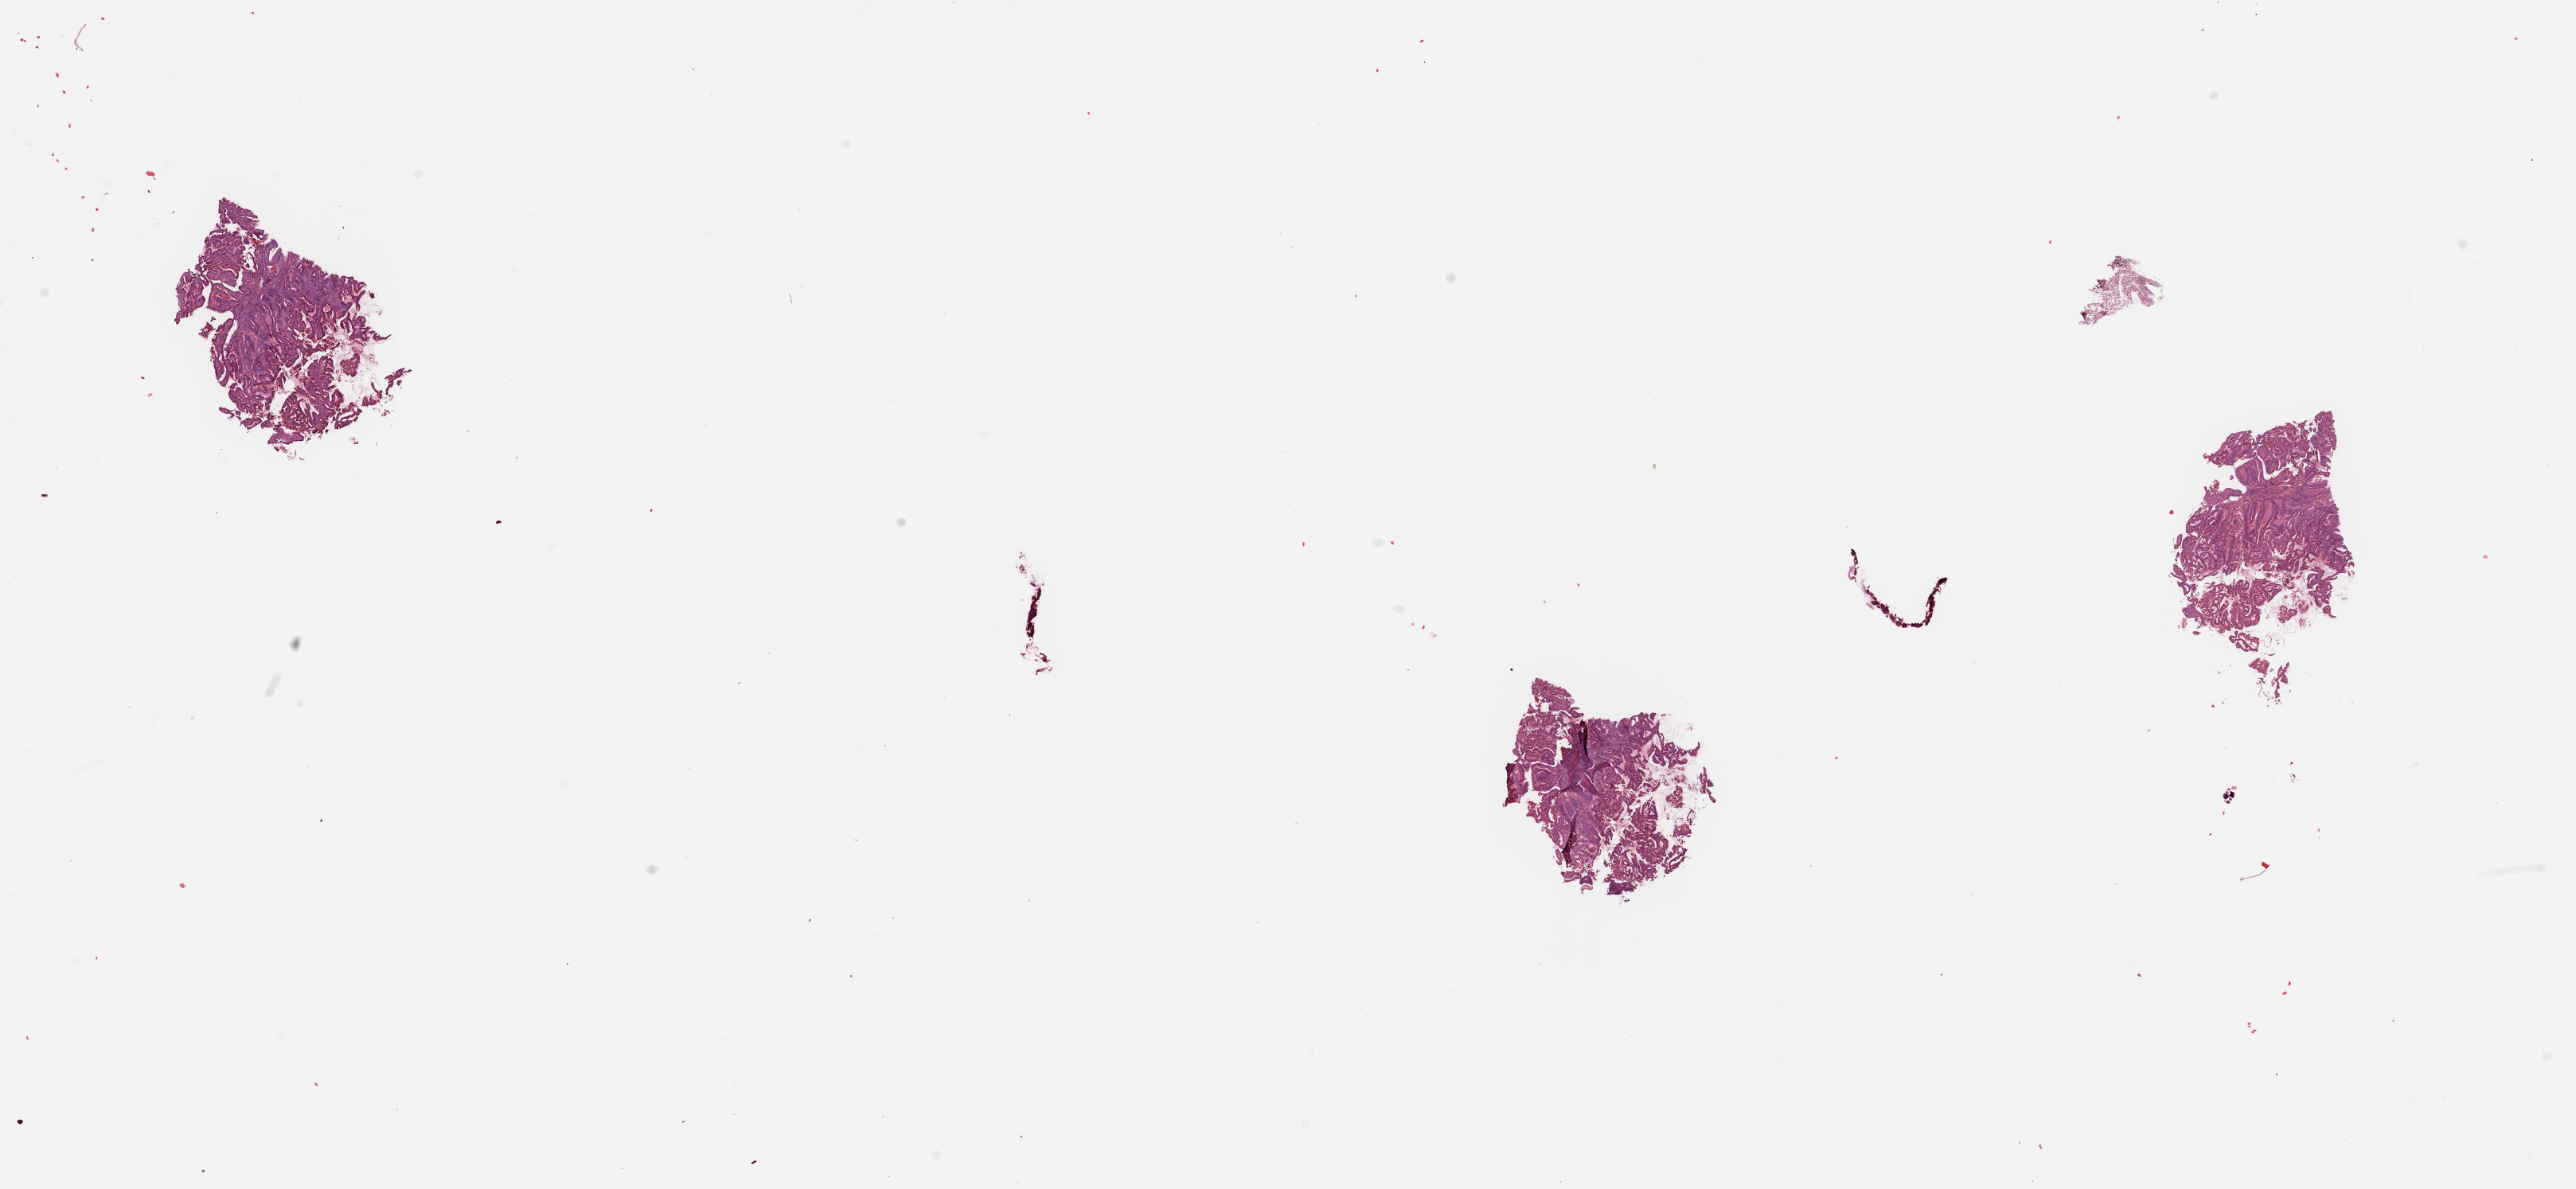
Whole-slide histology image, Hematoxylin and eosin (H&E) stained — whole scanned area (about 25.6 x 11.8 mm) shown as a low-resolution overview; tumour tissue sample, sampled site: uterus. Patient: female, age 77 years. Histologic grade: G2 (moderately differentiated). Pathologist review of this section (percent, as recorded): tumour nuclei 90%, necrosis 2%.
Histologic diagnosis: Endometrioid adenocarcinoma, NOS. AJCC pathologic stage: I. Primary tumour site (as recorded): anterior endometrium.